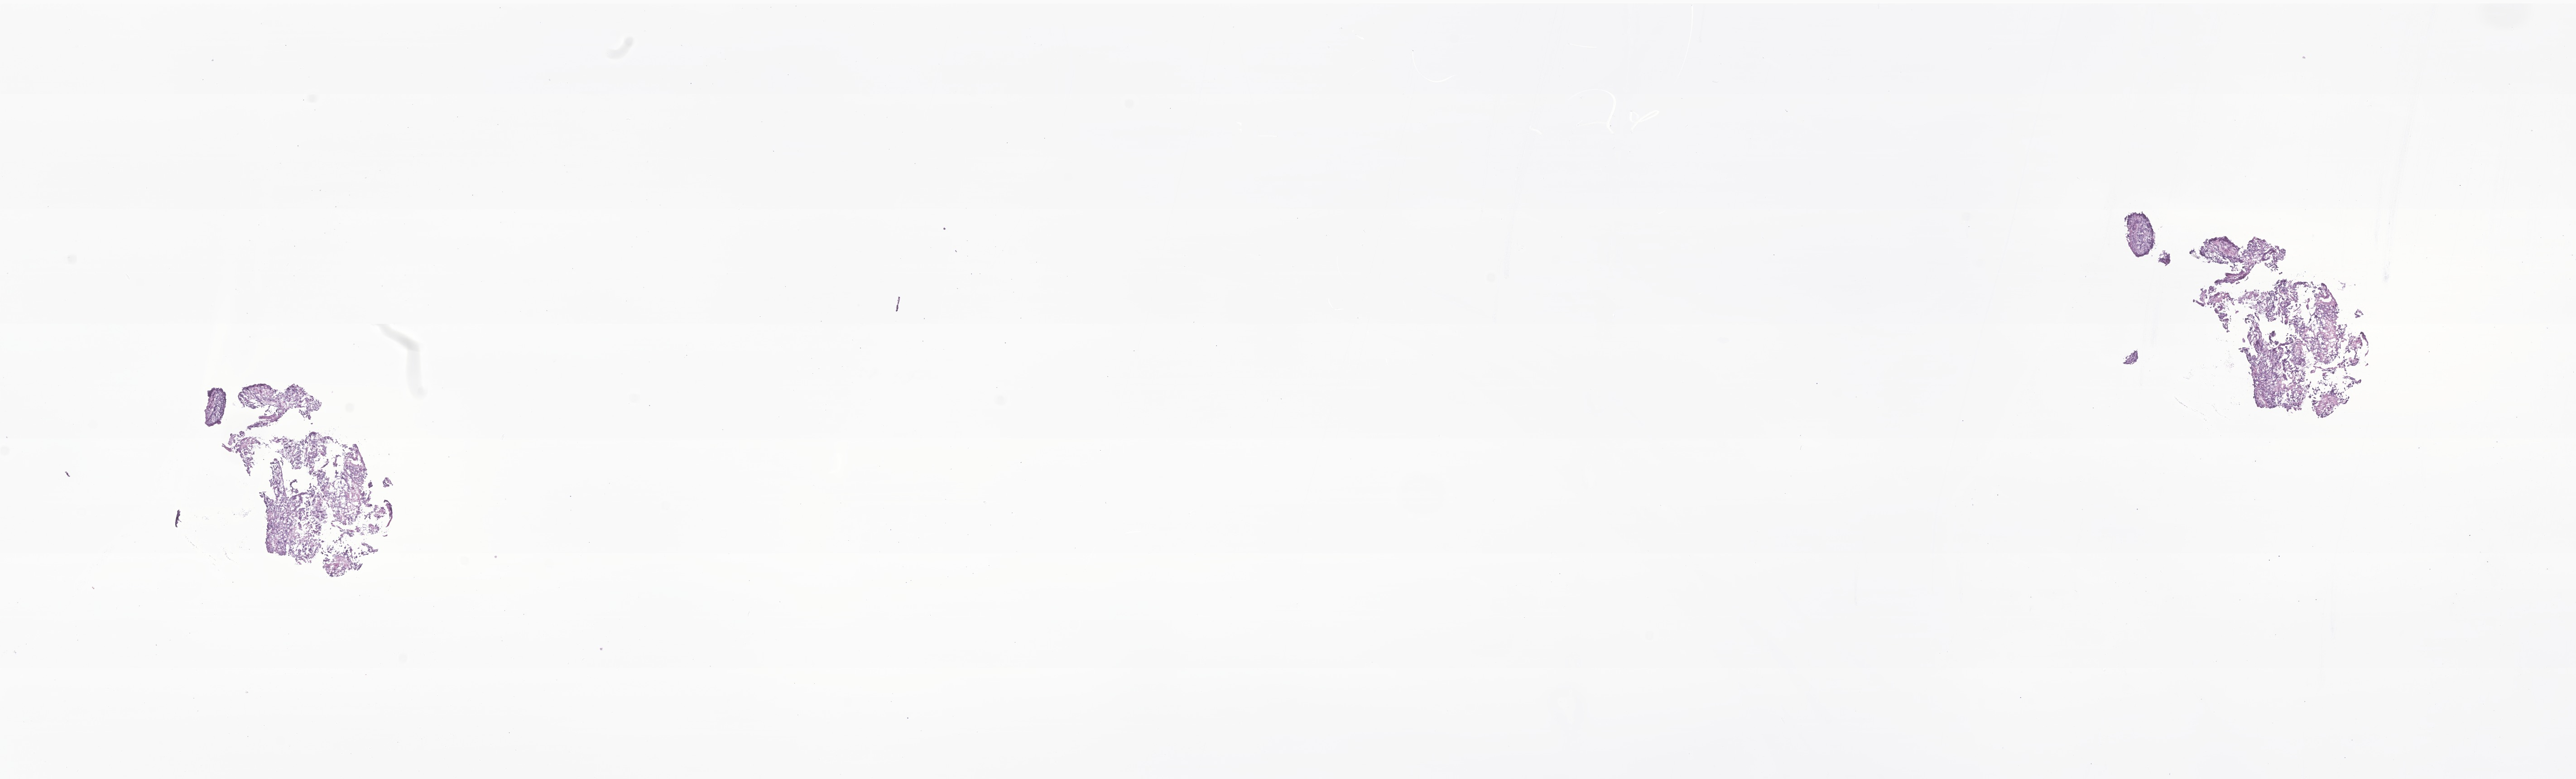
Whole-slide image, haematoxylin and eosin stain of tumor tissue from the nasopharynx, low-resolution overview of the scanned area, about 24.0 x 7.3 mm. Cryosection (OCT / tissue freezing medium). Male patient, age 80 months.
Recorded diagnosis: Embryonal rhabdomyosarcoma, NOS.